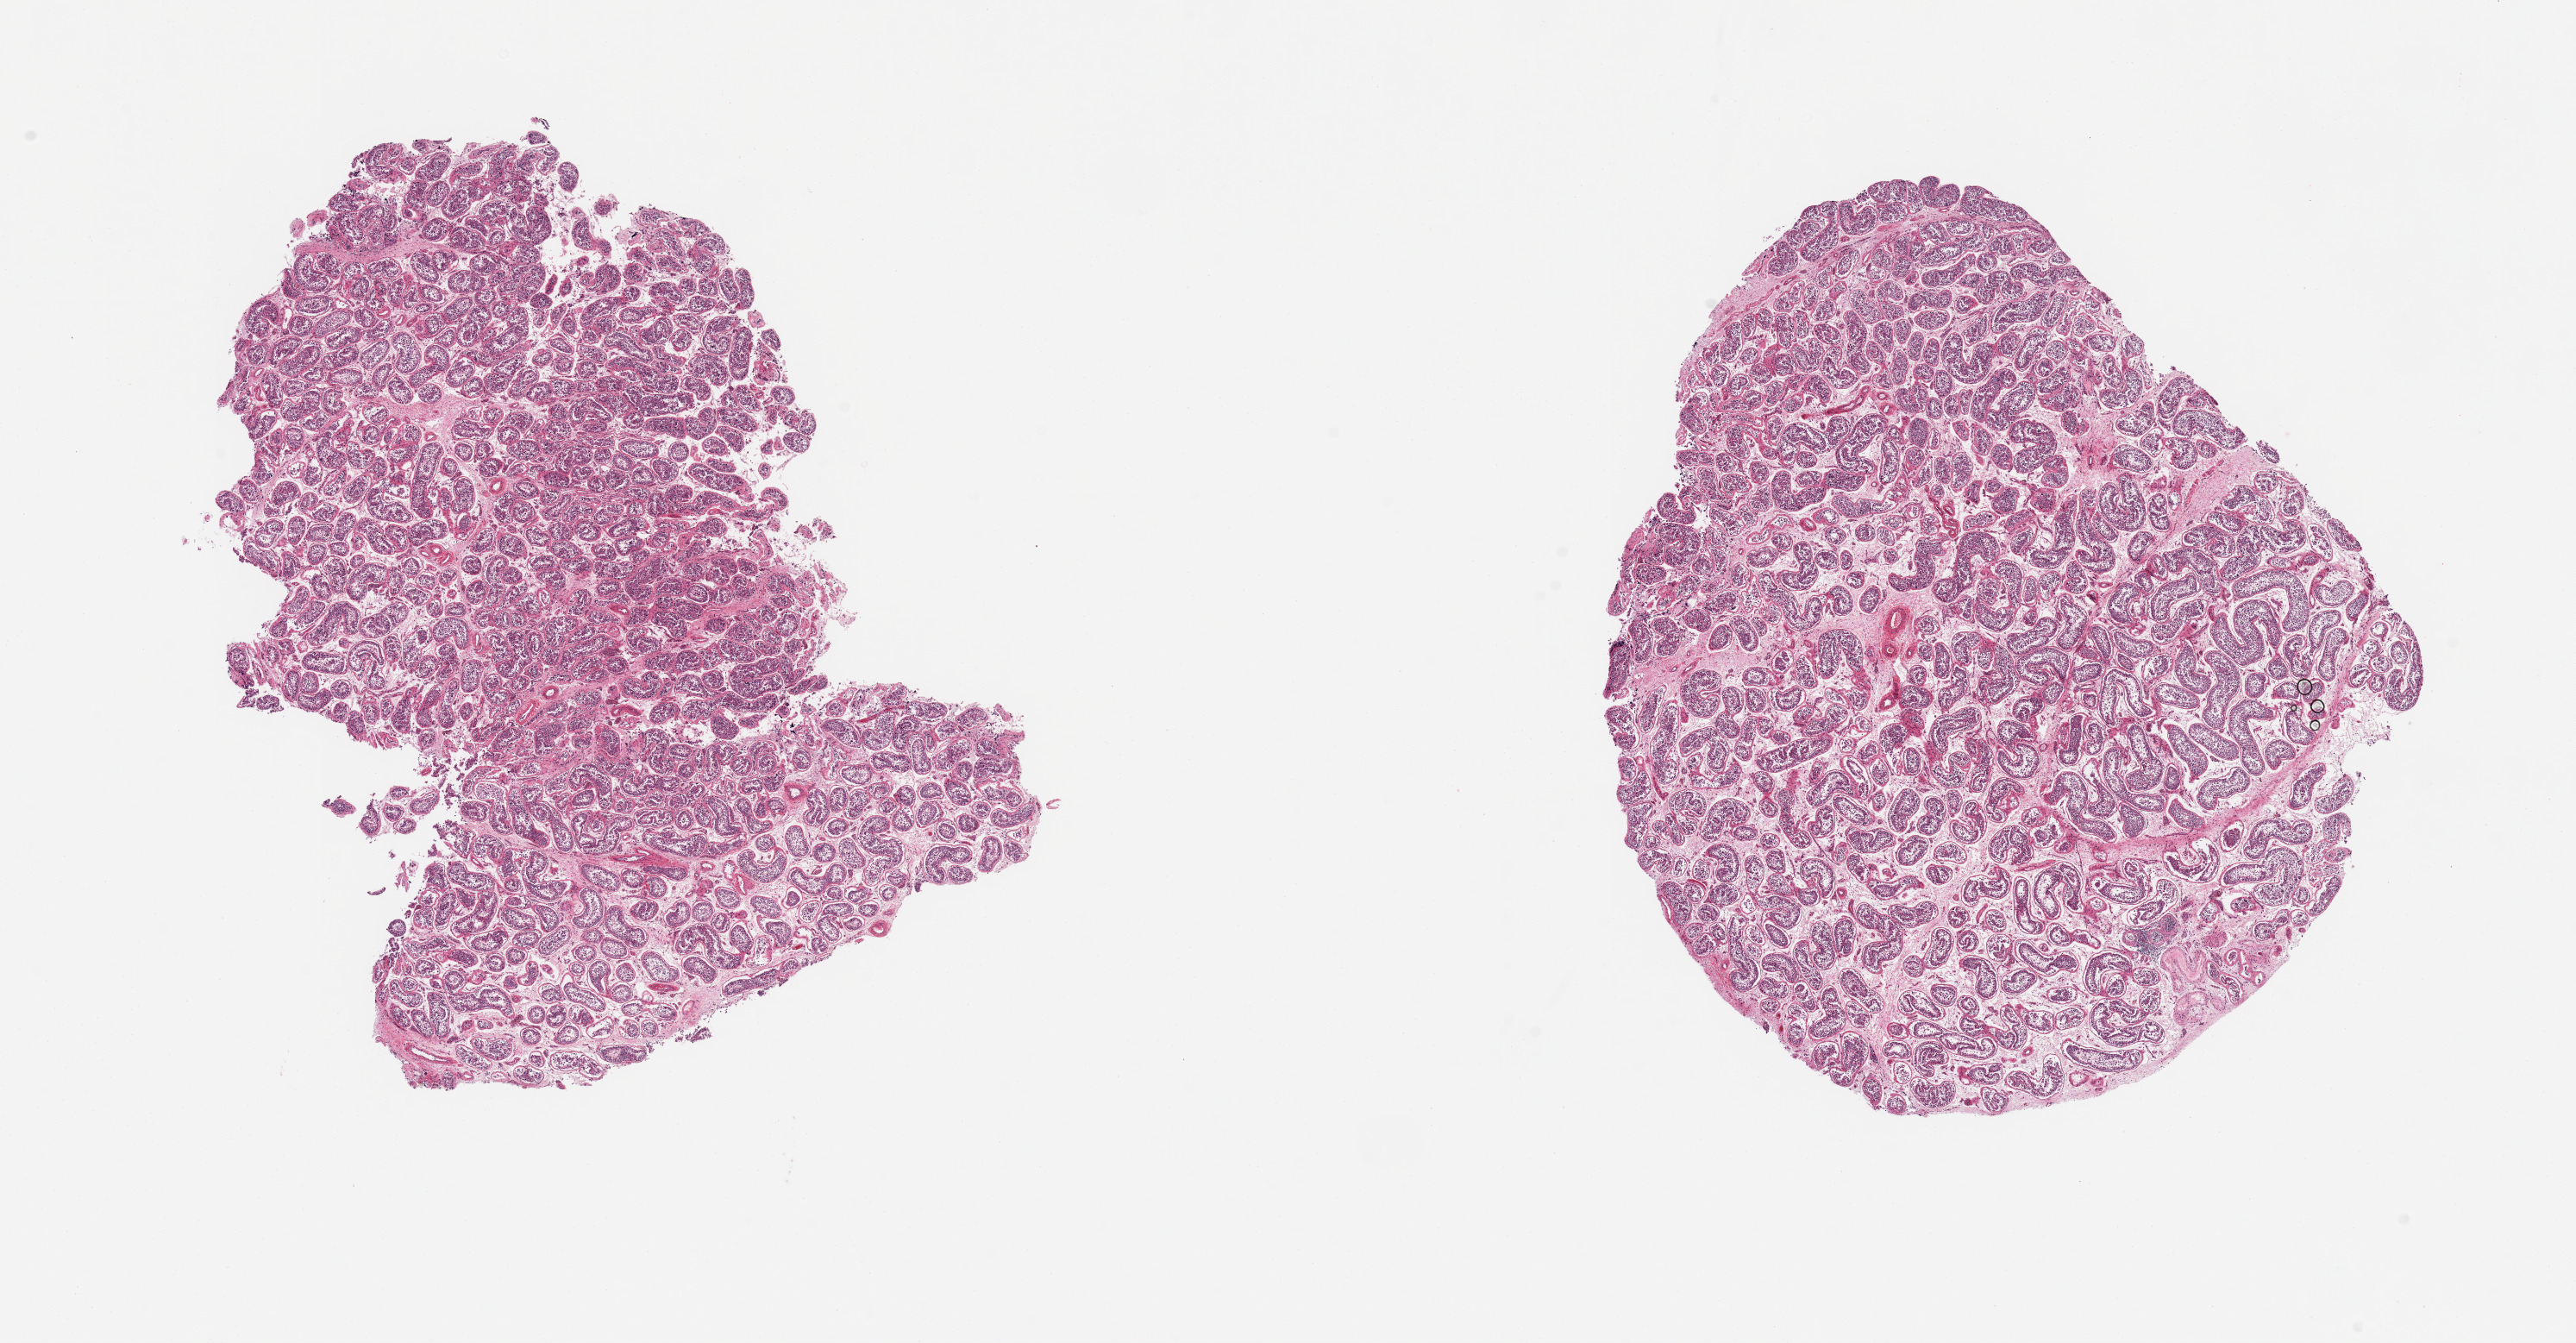
Whole-slide image, hematoxylin and eosin (H&E) stain, whole scanned area (about 23.6 x 12.3 mm) shown as a low-resolution overview. PAXgene-fixed, paraffin-embedded tissue. Sampled site (target tissue): testis. Donor tissue sample.
Reviewer comment on this tissue sample: 2 pieces; spermatogenesis present.